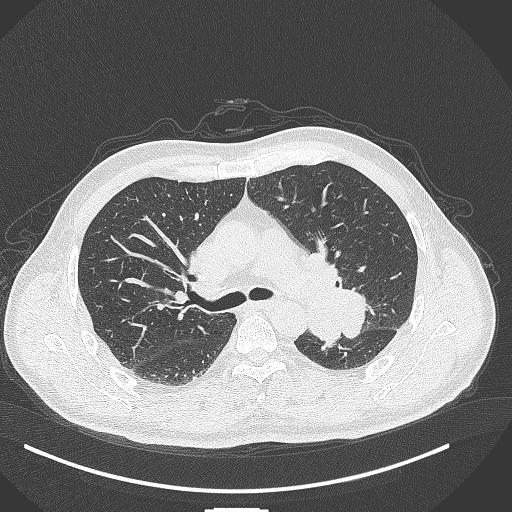
Chest CT, one axial slice. Slice 268 of 429 in the series (ordered by position). Reconstruction kernel B70f. Lung window (W 1500 / L -600 HU). 512 × 512 image matrix, field of view 400 × 400 mm. Patient: male, 55 years. From the clinical record (not read from this slice): clinical TNM (as recorded): T3 N0 M1c; histopathological grade: G3.
Structures marked on this image (rectangle marked by the reading radiologist):
- lung tumour (recorded histology: adenocarcinoma): bounding box (x1, y1, x2, y2) in pixels: (305, 275, 372, 348)